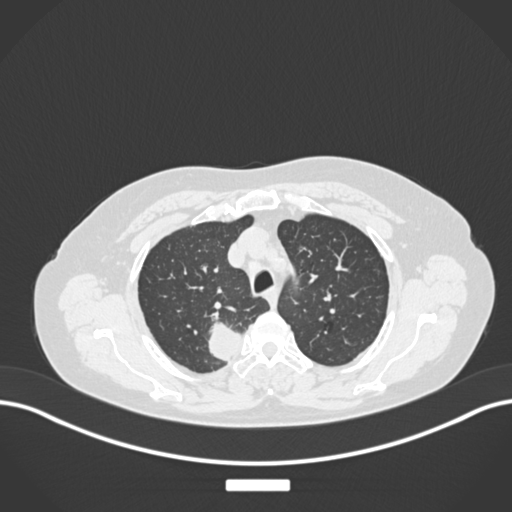
Chest CT, one axial slice. Slice 204 of 237 in the series (ordered by position). Reconstruction kernel B30f. Lung window (W 1500 / L -600 HU). 1 mm slice thickness. 512 × 512 image matrix, field of view 400 × 400 mm. Patient: female, 62 years. Case-level facts recorded for this patient, not image findings: clinical TNM (as recorded): T1c N1 M0.
Structures marked on this image (rectangle marked by the reading radiologist):
- lung tumour (recorded histology: squamous cell carcinoma): box from (x=206, y=318) to (x=247, y=369) px